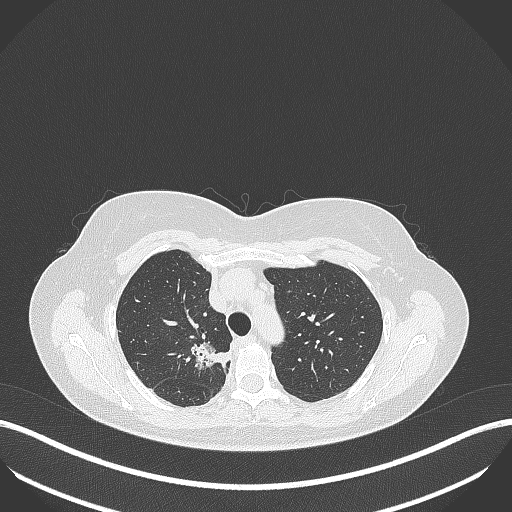
Chest CT, one axial slice; position 298 of 386 along the scan axis; lung window (W 1500 / L -600 HU); 1 mm slice thickness; 512 × 512 image matrix, field of view 400 × 400 mm. Female patient, age 65 years. From the clinical record (not read from this slice): clinical TNM (as recorded): T1b N0 M0; histopathological grade: G2.
Structures marked on this image (bounding box drawn by a radiologist):
- lung tumour (recorded histology: adenocarcinoma): bounding box (x1, y1, x2, y2) in pixels: (188, 337, 234, 373)